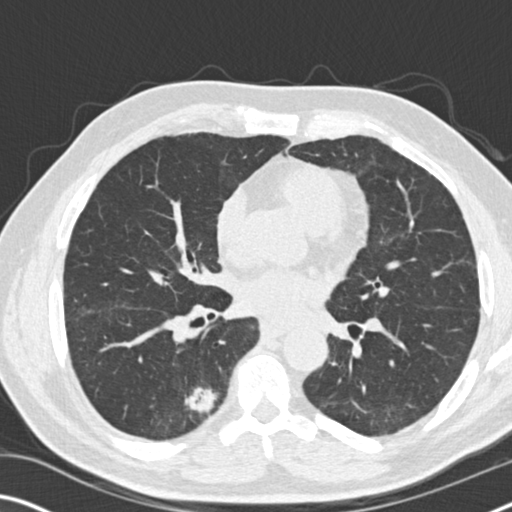
Axial slice from a low-dose chest CT screening exam, baseline screening round, lung window (W 1500 / L -600 HU), 2 mm slice thickness, standard (soft-tissue) reconstruction kernel (B30f), 120 kVp, 512 × 512 image matrix. Male, age 71 years at enrolment. Current smoker at enrolment.
Expert reader's lesion annotation, bounding box <159,372,228,433> (left, top, right, bottom; pixels). The screening reader recorded 2 non-calcified nodules or masses ≥4 mm on this exam (right lower lobe, left lower lobe); which of them this box marks is not recorded.